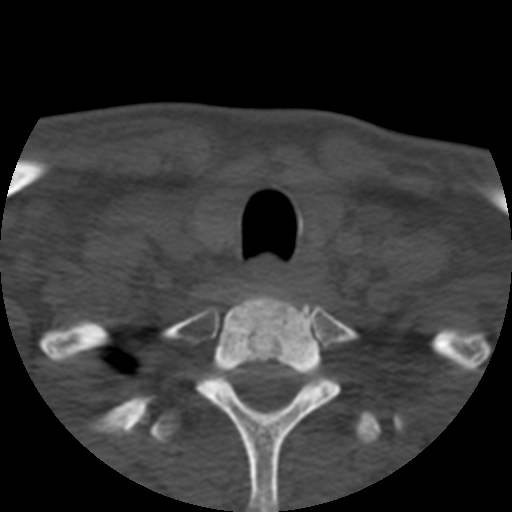
CT including the spine, one axial slice; slice 446 of 508 in the series (ordered by position); reconstruction kernel STANDARD; bone window (W 1800 / L 400 HU); 1.25 mm slice thickness; 512 × 512 image matrix, field of view 160 × 160 mm. Patient age 57 years. From the clinical record (not read from this slice): primary cancer: prostate.
Annotated regions visible in this slice (semi-automatic segmentation, software-assisted and operator-edited):
- T1 vertebra: bounding box [x1, y1, x2, y2] px = [100, 287, 381, 512]
- T2 vertebra: [148, 408, 404, 451]